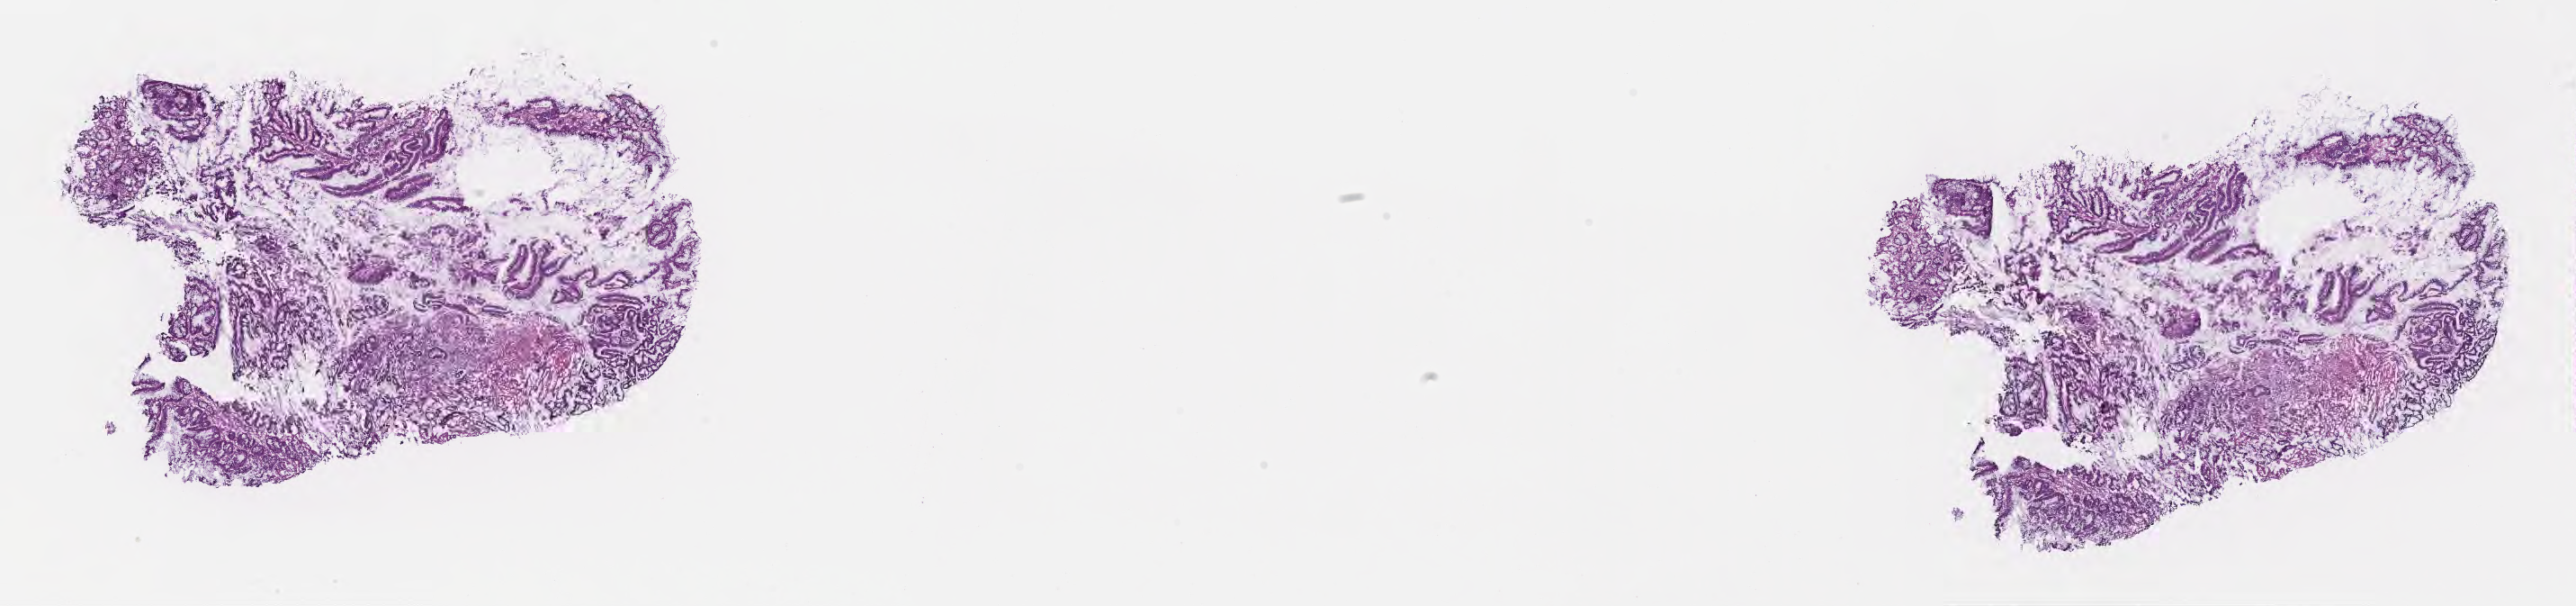
Whole-slide image, H&E stain, a low-resolution overview of the entire scanned area, about 23.1 x 5.4 mm, frozen section (tissue freezing medium), premalignant lesion from a patient with serrated adenoma, NOS, anatomic site: transverse colon. Male, age 54 years at initial diagnosis. Pathologist review of this section (percent, as recorded): tumor cells 25%, tumor nuclei 25%, stromal cells 75%, necrosis 0%, normal cells 0%. Infiltration values recorded for this section: lymphocyte infiltration 5%, monocyte infiltration 2%, neutrophil infiltration 7%.
- this section: sample classed premalignant; the patient's recorded diagnosis is given above
- section: top of the tissue portion